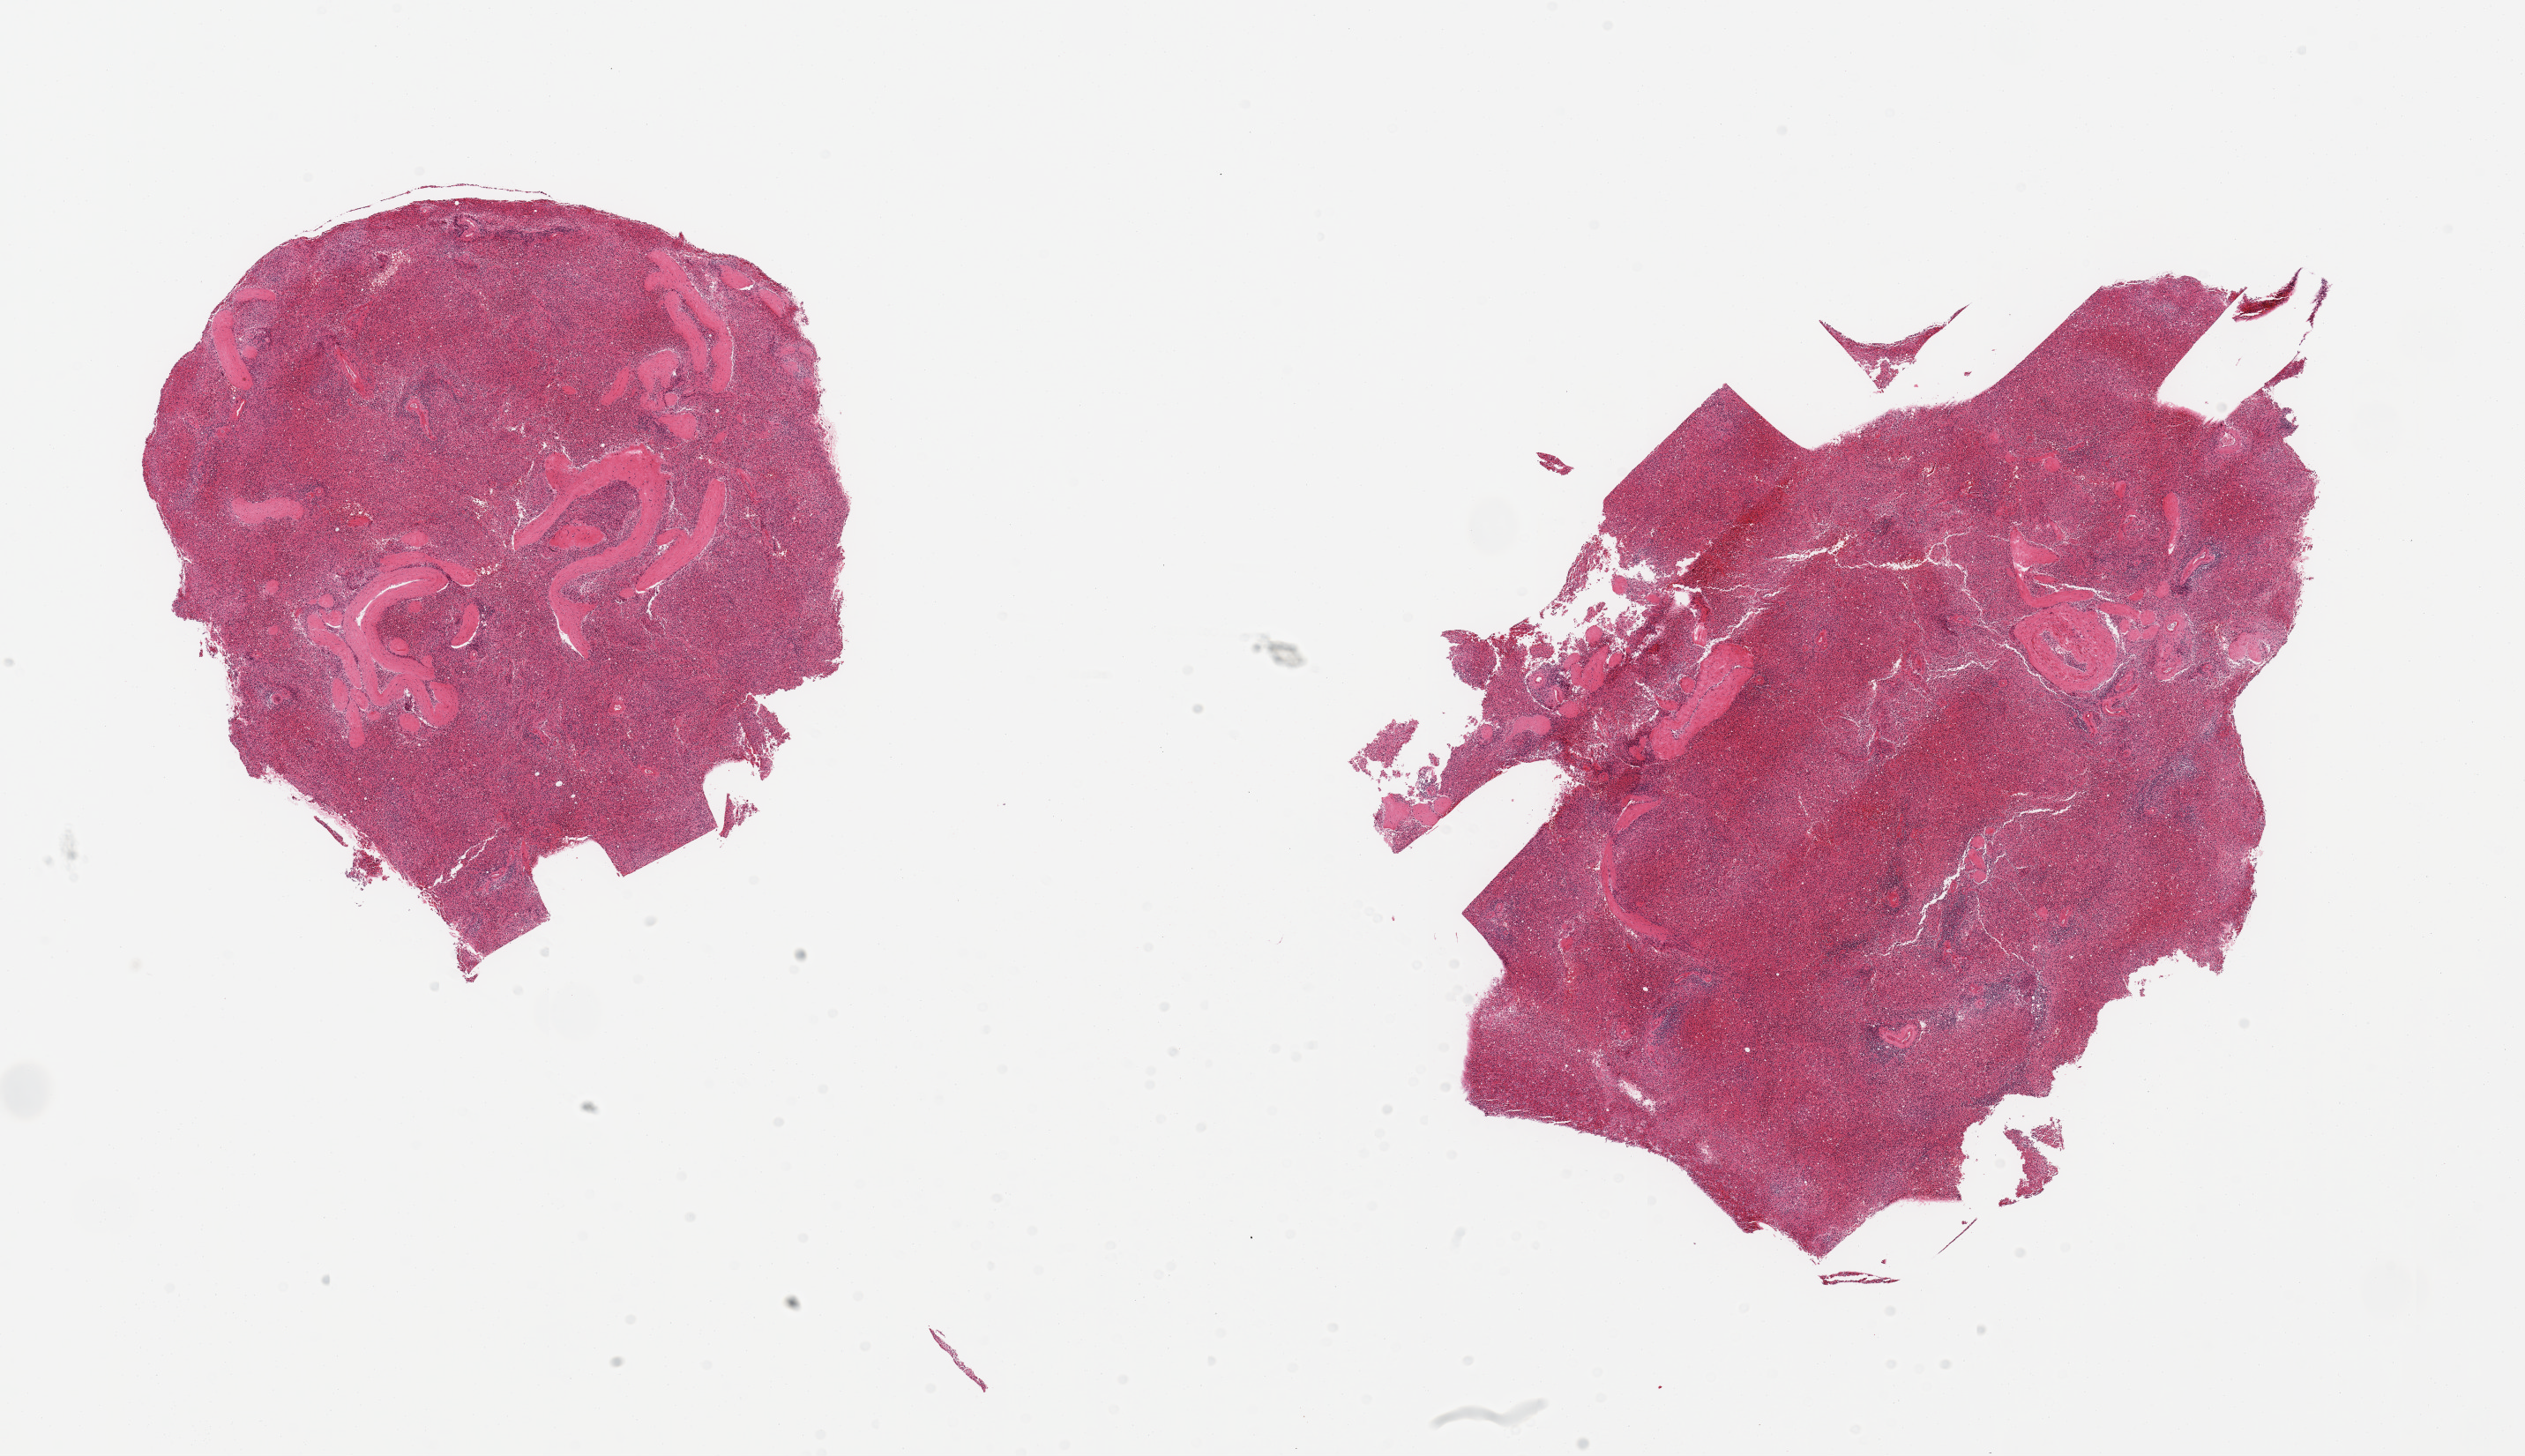
Digitized hematoxylin and eosin (H&E)-stained section — a low-resolution overview of the entire scanned area, about 22.6 x 13.1 mm; PAXgene-fixed, paraffin-embedded tissue; section of spleen (target tissue); donor tissue sample. Donor sex: male.
Reviewer comment on this tissue sample: 2 pieces; moderate congestion.